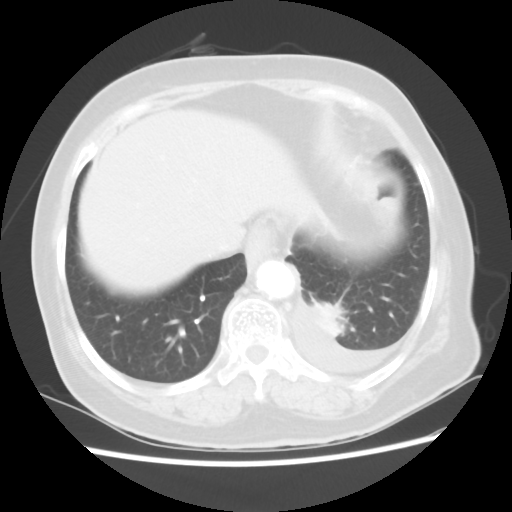
Chest CT, one axial slice. Reconstruction kernel STANDARD. 100 kVp. Lung window (W 1500 / L -600 HU). 5 mm slice thickness. 512 × 512 image matrix, field of view 343 × 343 mm. Female patient, age 68 years. From the clinical record (not read from this slice): clinical TNM (as recorded): T1c N0 M1.
Outlined on this slice (rectangle marked by the reading radiologist):
- lung tumour (recorded histology: adenocarcinoma): bounding box [x1, y1, x2, y2] px = [311, 298, 355, 345]